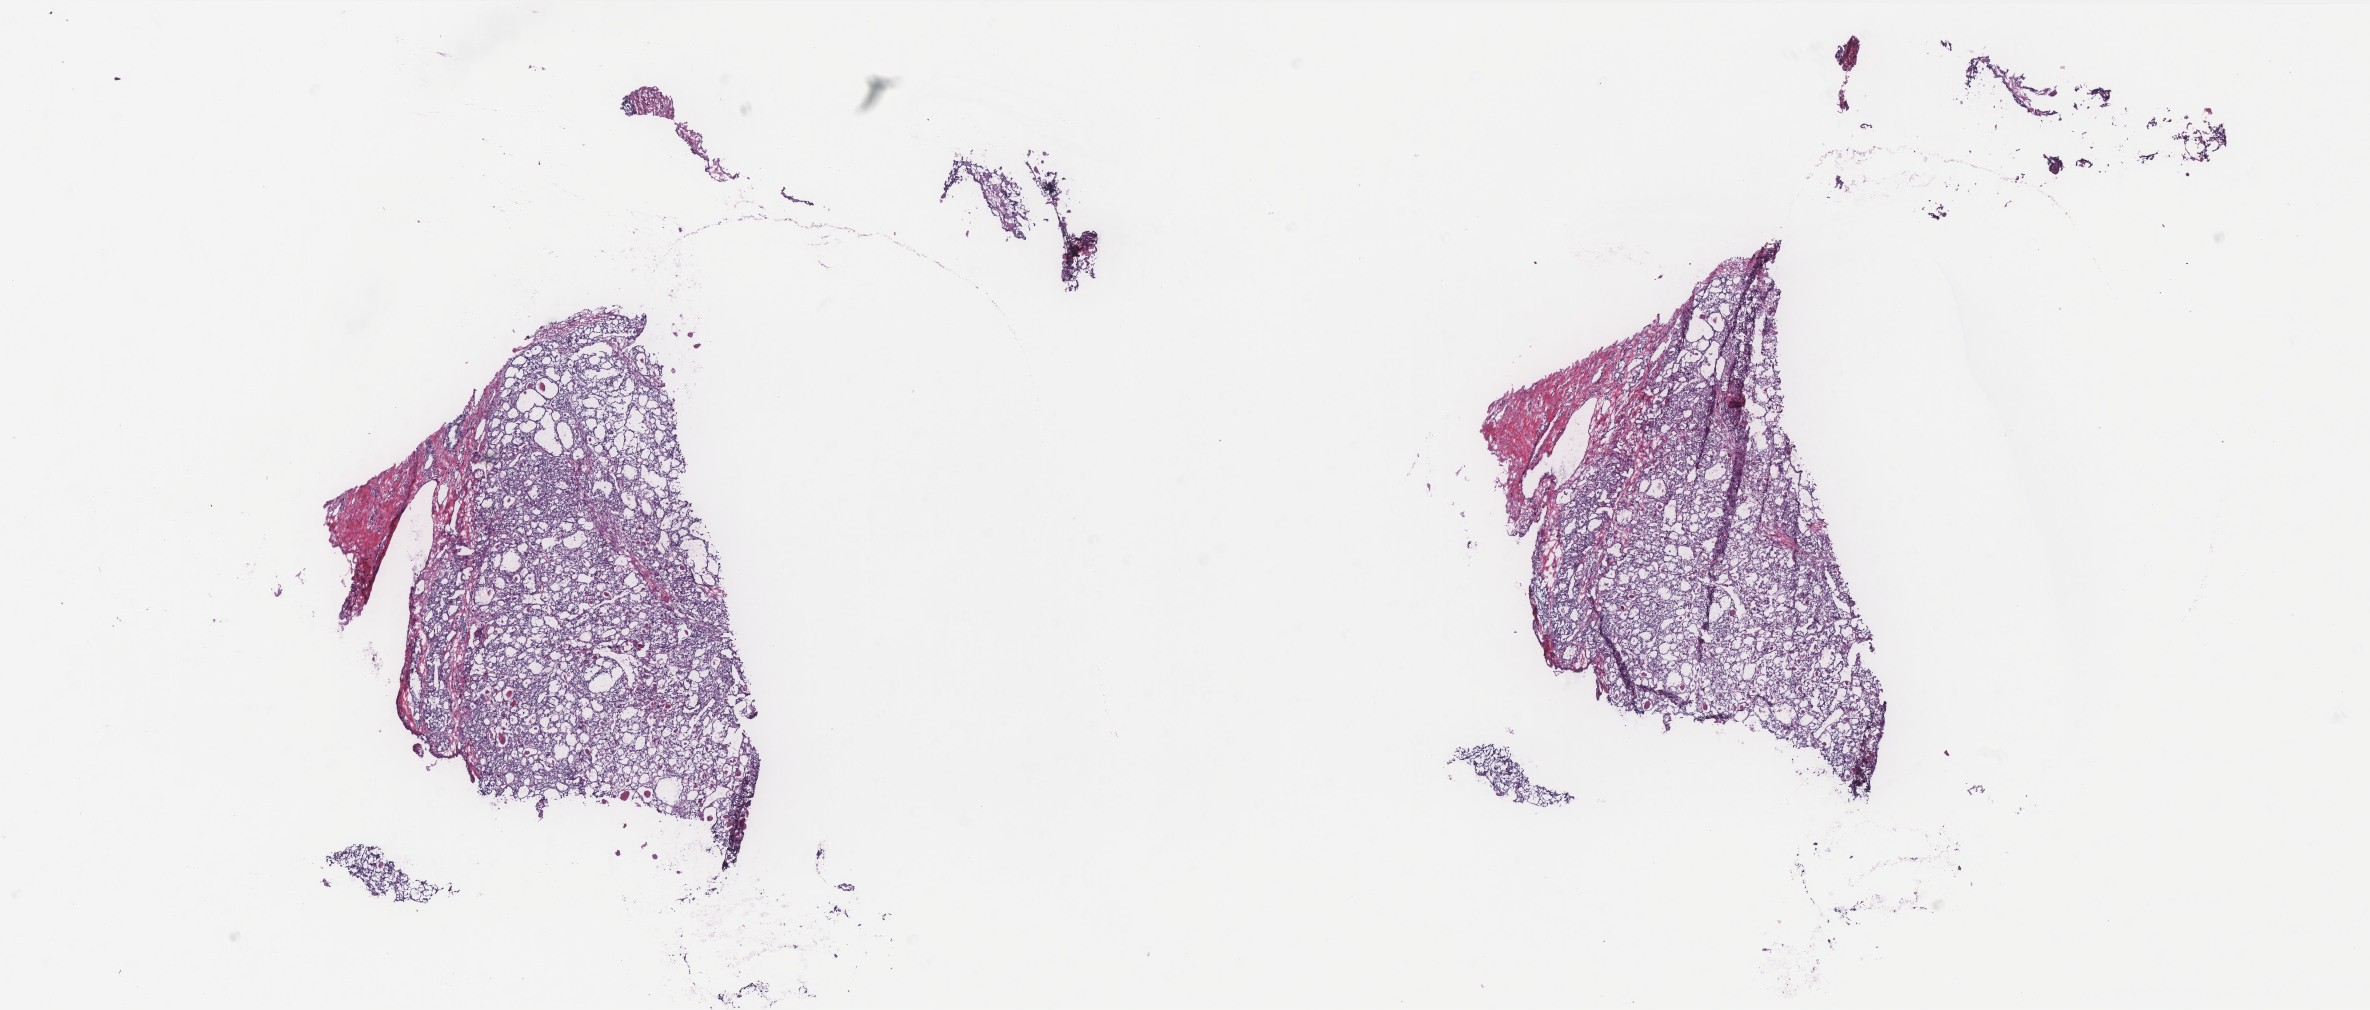
Whole-slide histology image, H&E — shown as a low-resolution overview of the whole scanned area (about 19.0 x 8.1 mm, acquisition: 40x scan), frozen section from the bottom of the tissue portion, thyroid, primary tumour sample. Male patient; age at initial diagnosis 65 years.
Pathologic diagnosis: Papillary adenocarcinoma, NOS (thyroid gland).